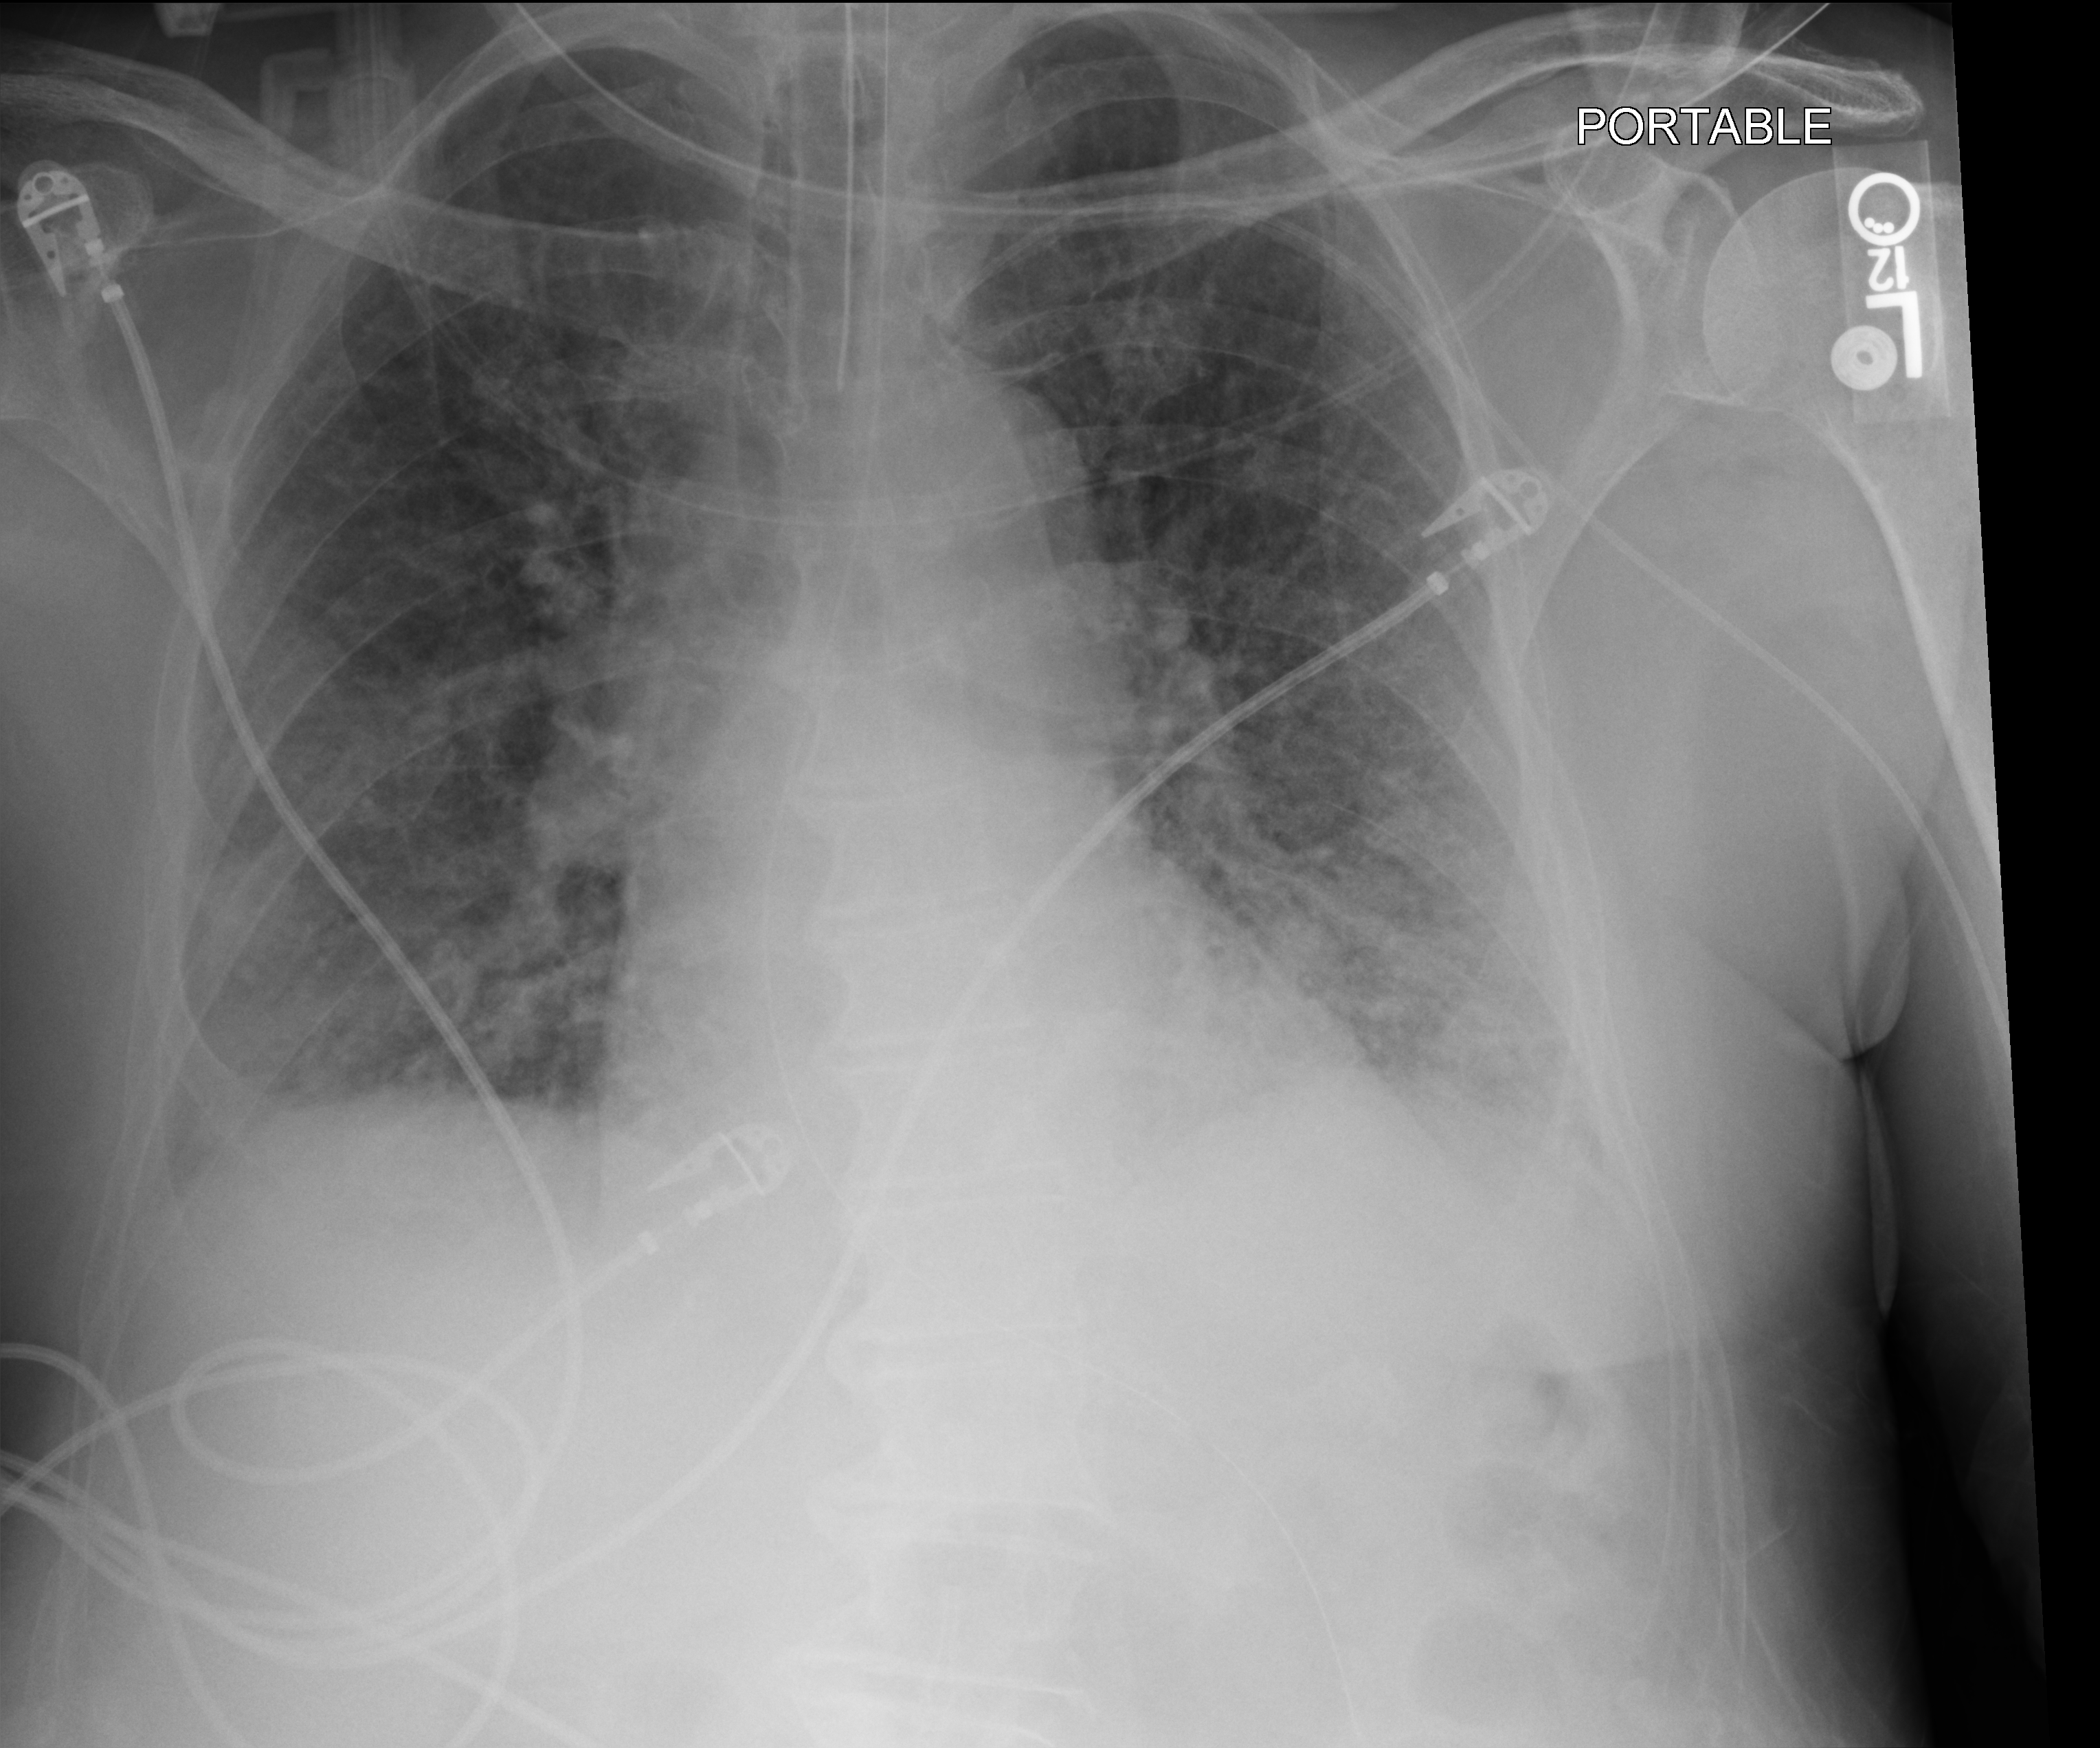
Bedside chest radiograph (computed radiography); anteroposterior (AP) projection. Male patient hospitalised with COVID-19, age 75–90 years.
Hospital-stay facts (about this admission, not read from this image; timing relative to this image not recorded): mechanically ventilated during this hospital stay: yes; admitted to intensive care during this hospital stay: yes; length of hospital stay: 47 days.